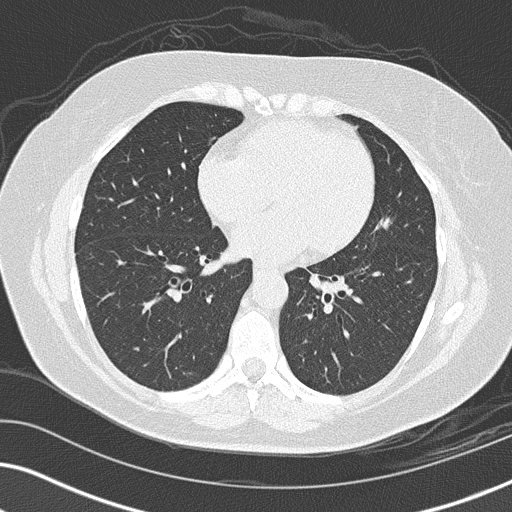
Chest CT (low-dose screening protocol), one axial image. Third annual screen. Lung window (W 1500 / L -600 HU). Lung (sharp) reconstruction kernel (B50f). 512 × 512 image matrix. Female, age 56 years at enrolment. Former smoker at enrolment.
Lesion marked by an expert reader, box from (x=354, y=200) to (x=412, y=252) px. Screening reader's record for this exam (one nodule recorded; not confirmed to be the boxed lesion): non-calcified nodule or mass ≥4 mm, lingula, 14 × 14 mm, spiculated (stellate) margins, soft tissue attenuation, pre-existing on the prior screen: yes; interval growth: yes. Official screen result: positive, other. Lung cancer was diagnosed 86 days after this screen: adenocarcinoma, NOS, left upper lobe, poorly differentiated (G3), stage IIIA (AJCC 6th edition), 15 mm at pathology.